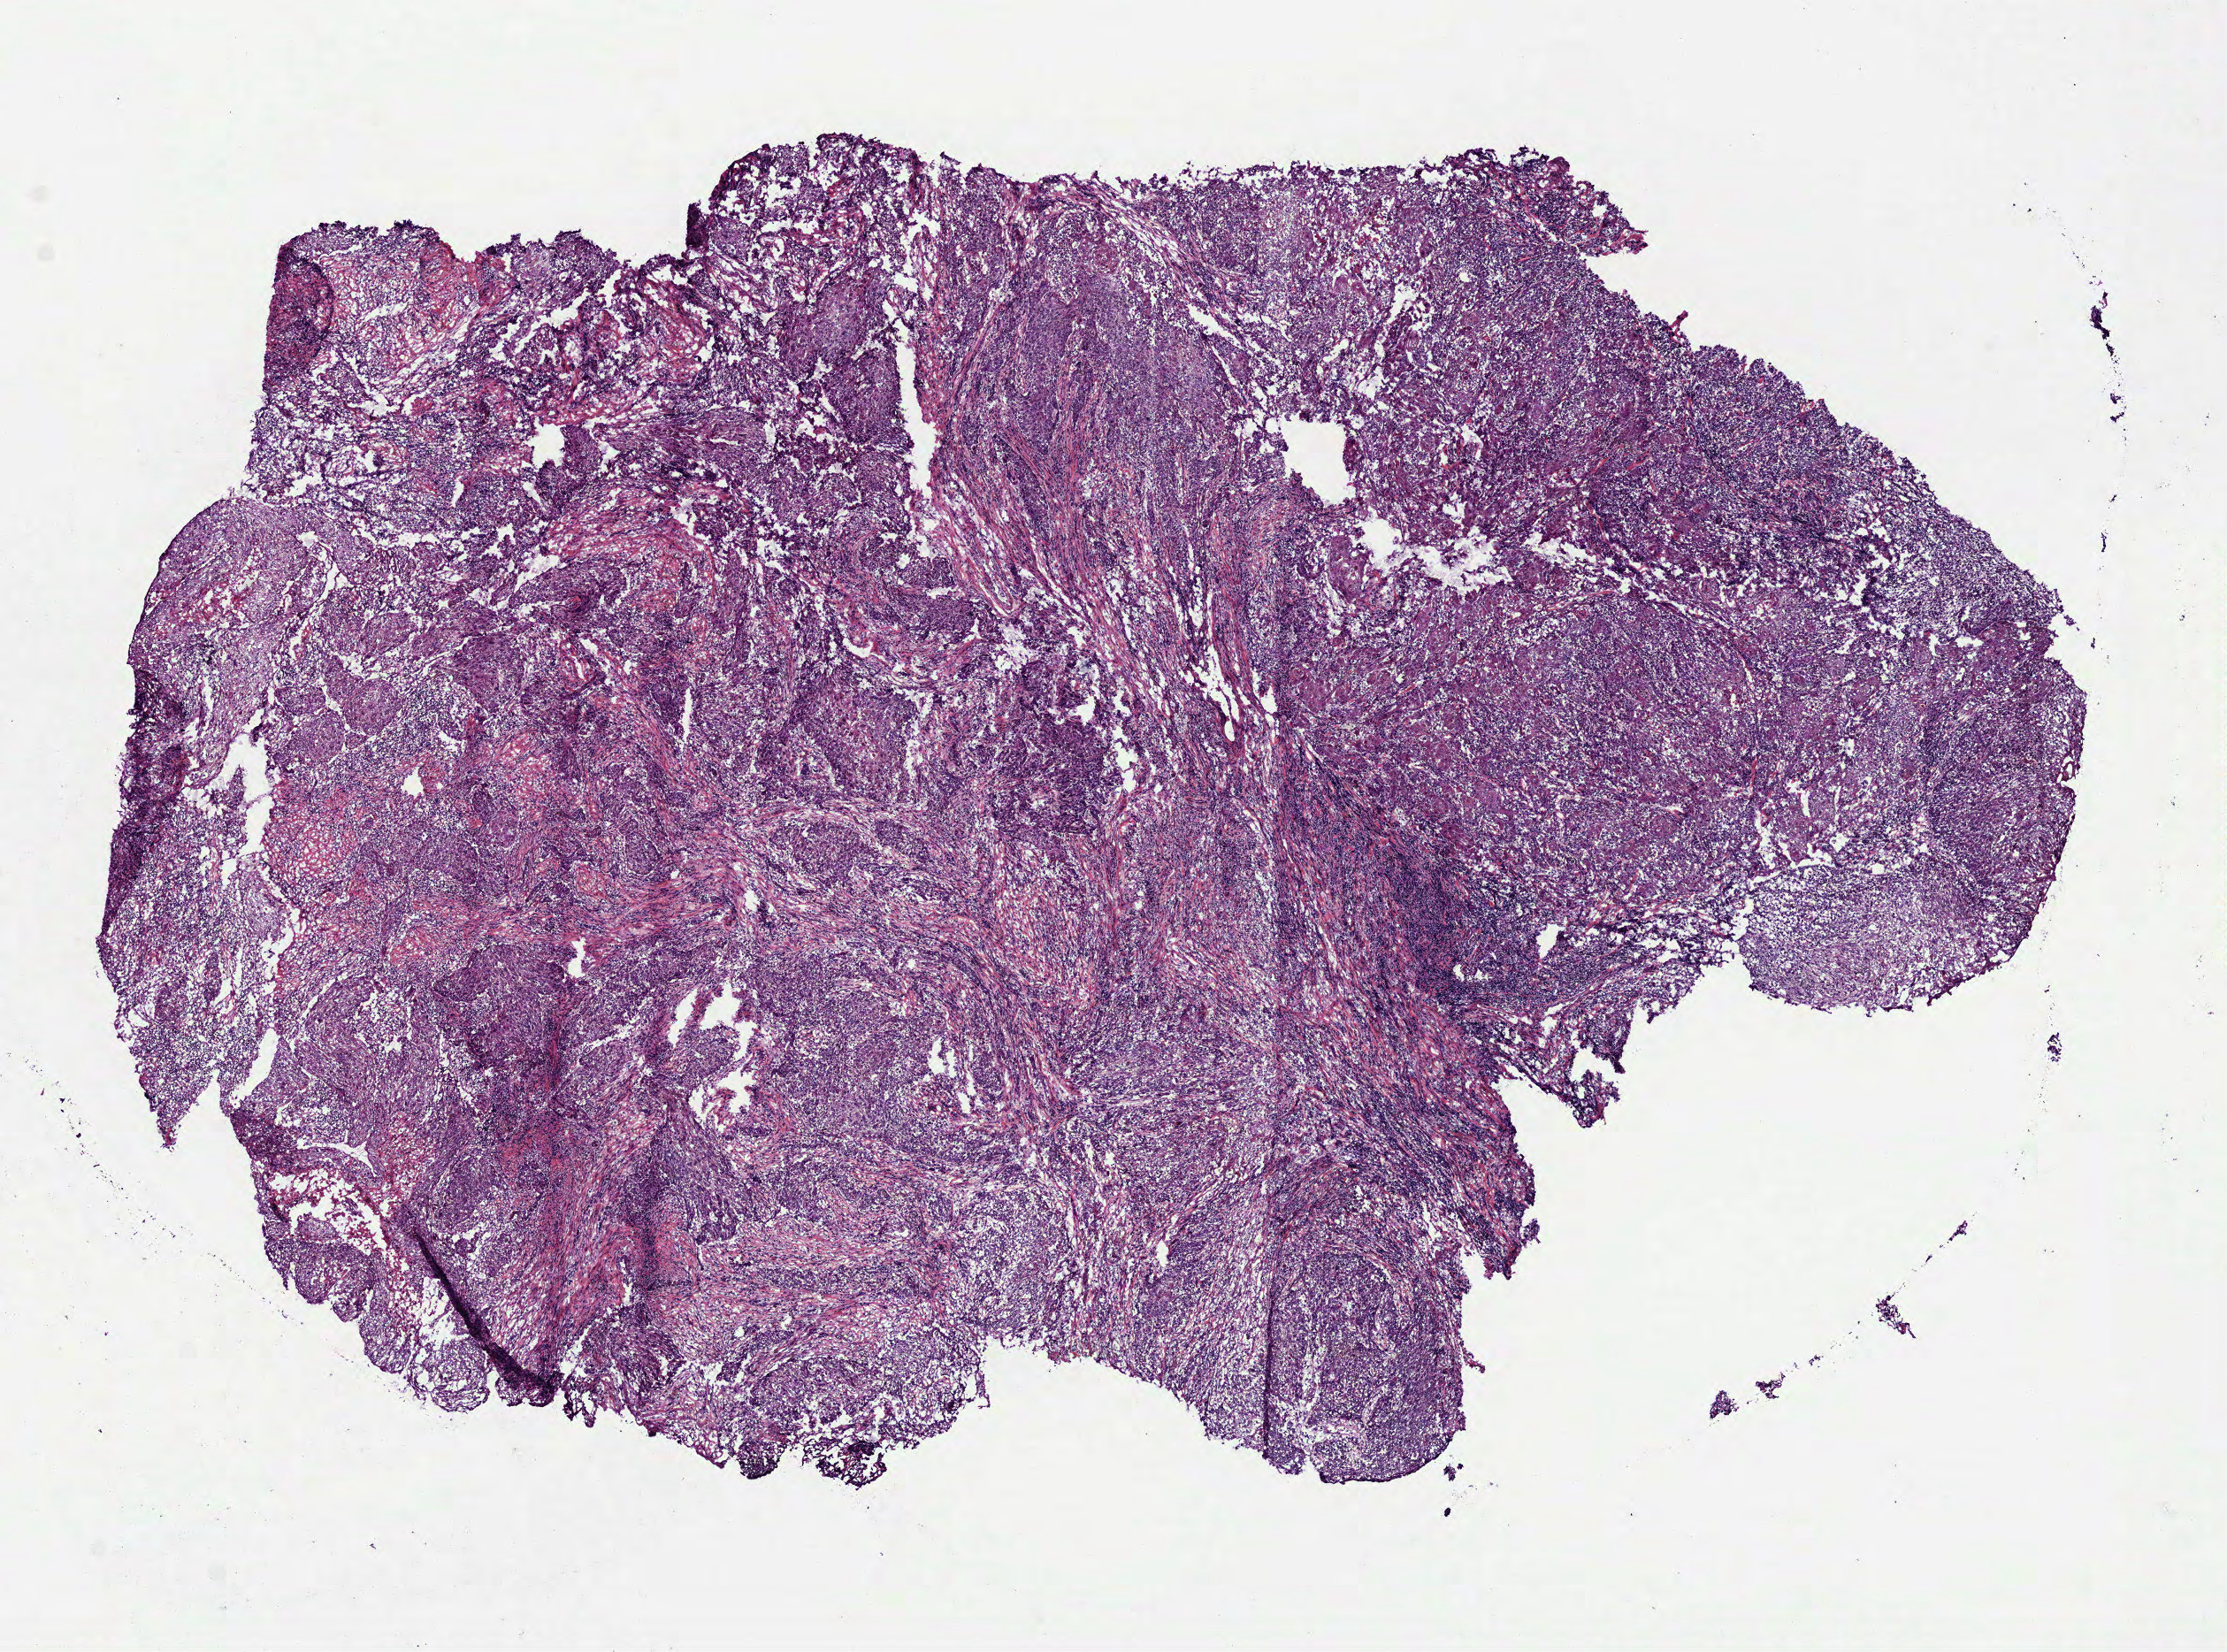
H&E whole-slide image, shown as a low-resolution overview of the whole scanned area (about 10.2 x 7.5 mm, from a 40x scan); frozen section from the top of the tissue portion; sample: primary tumour, head and neck. Male, age 56 years at initial diagnosis. Histologic grade: G3 (poorly differentiated). Slide review estimates, as recorded: tumour cells 82%, tumour nuclei 65%, normal cells 0%, stromal cells 15%, necrosis 3%.
* AJCC pathologic stage: IVA
* diagnosis: Squamous cell carcinoma, NOS (gum, NOS)